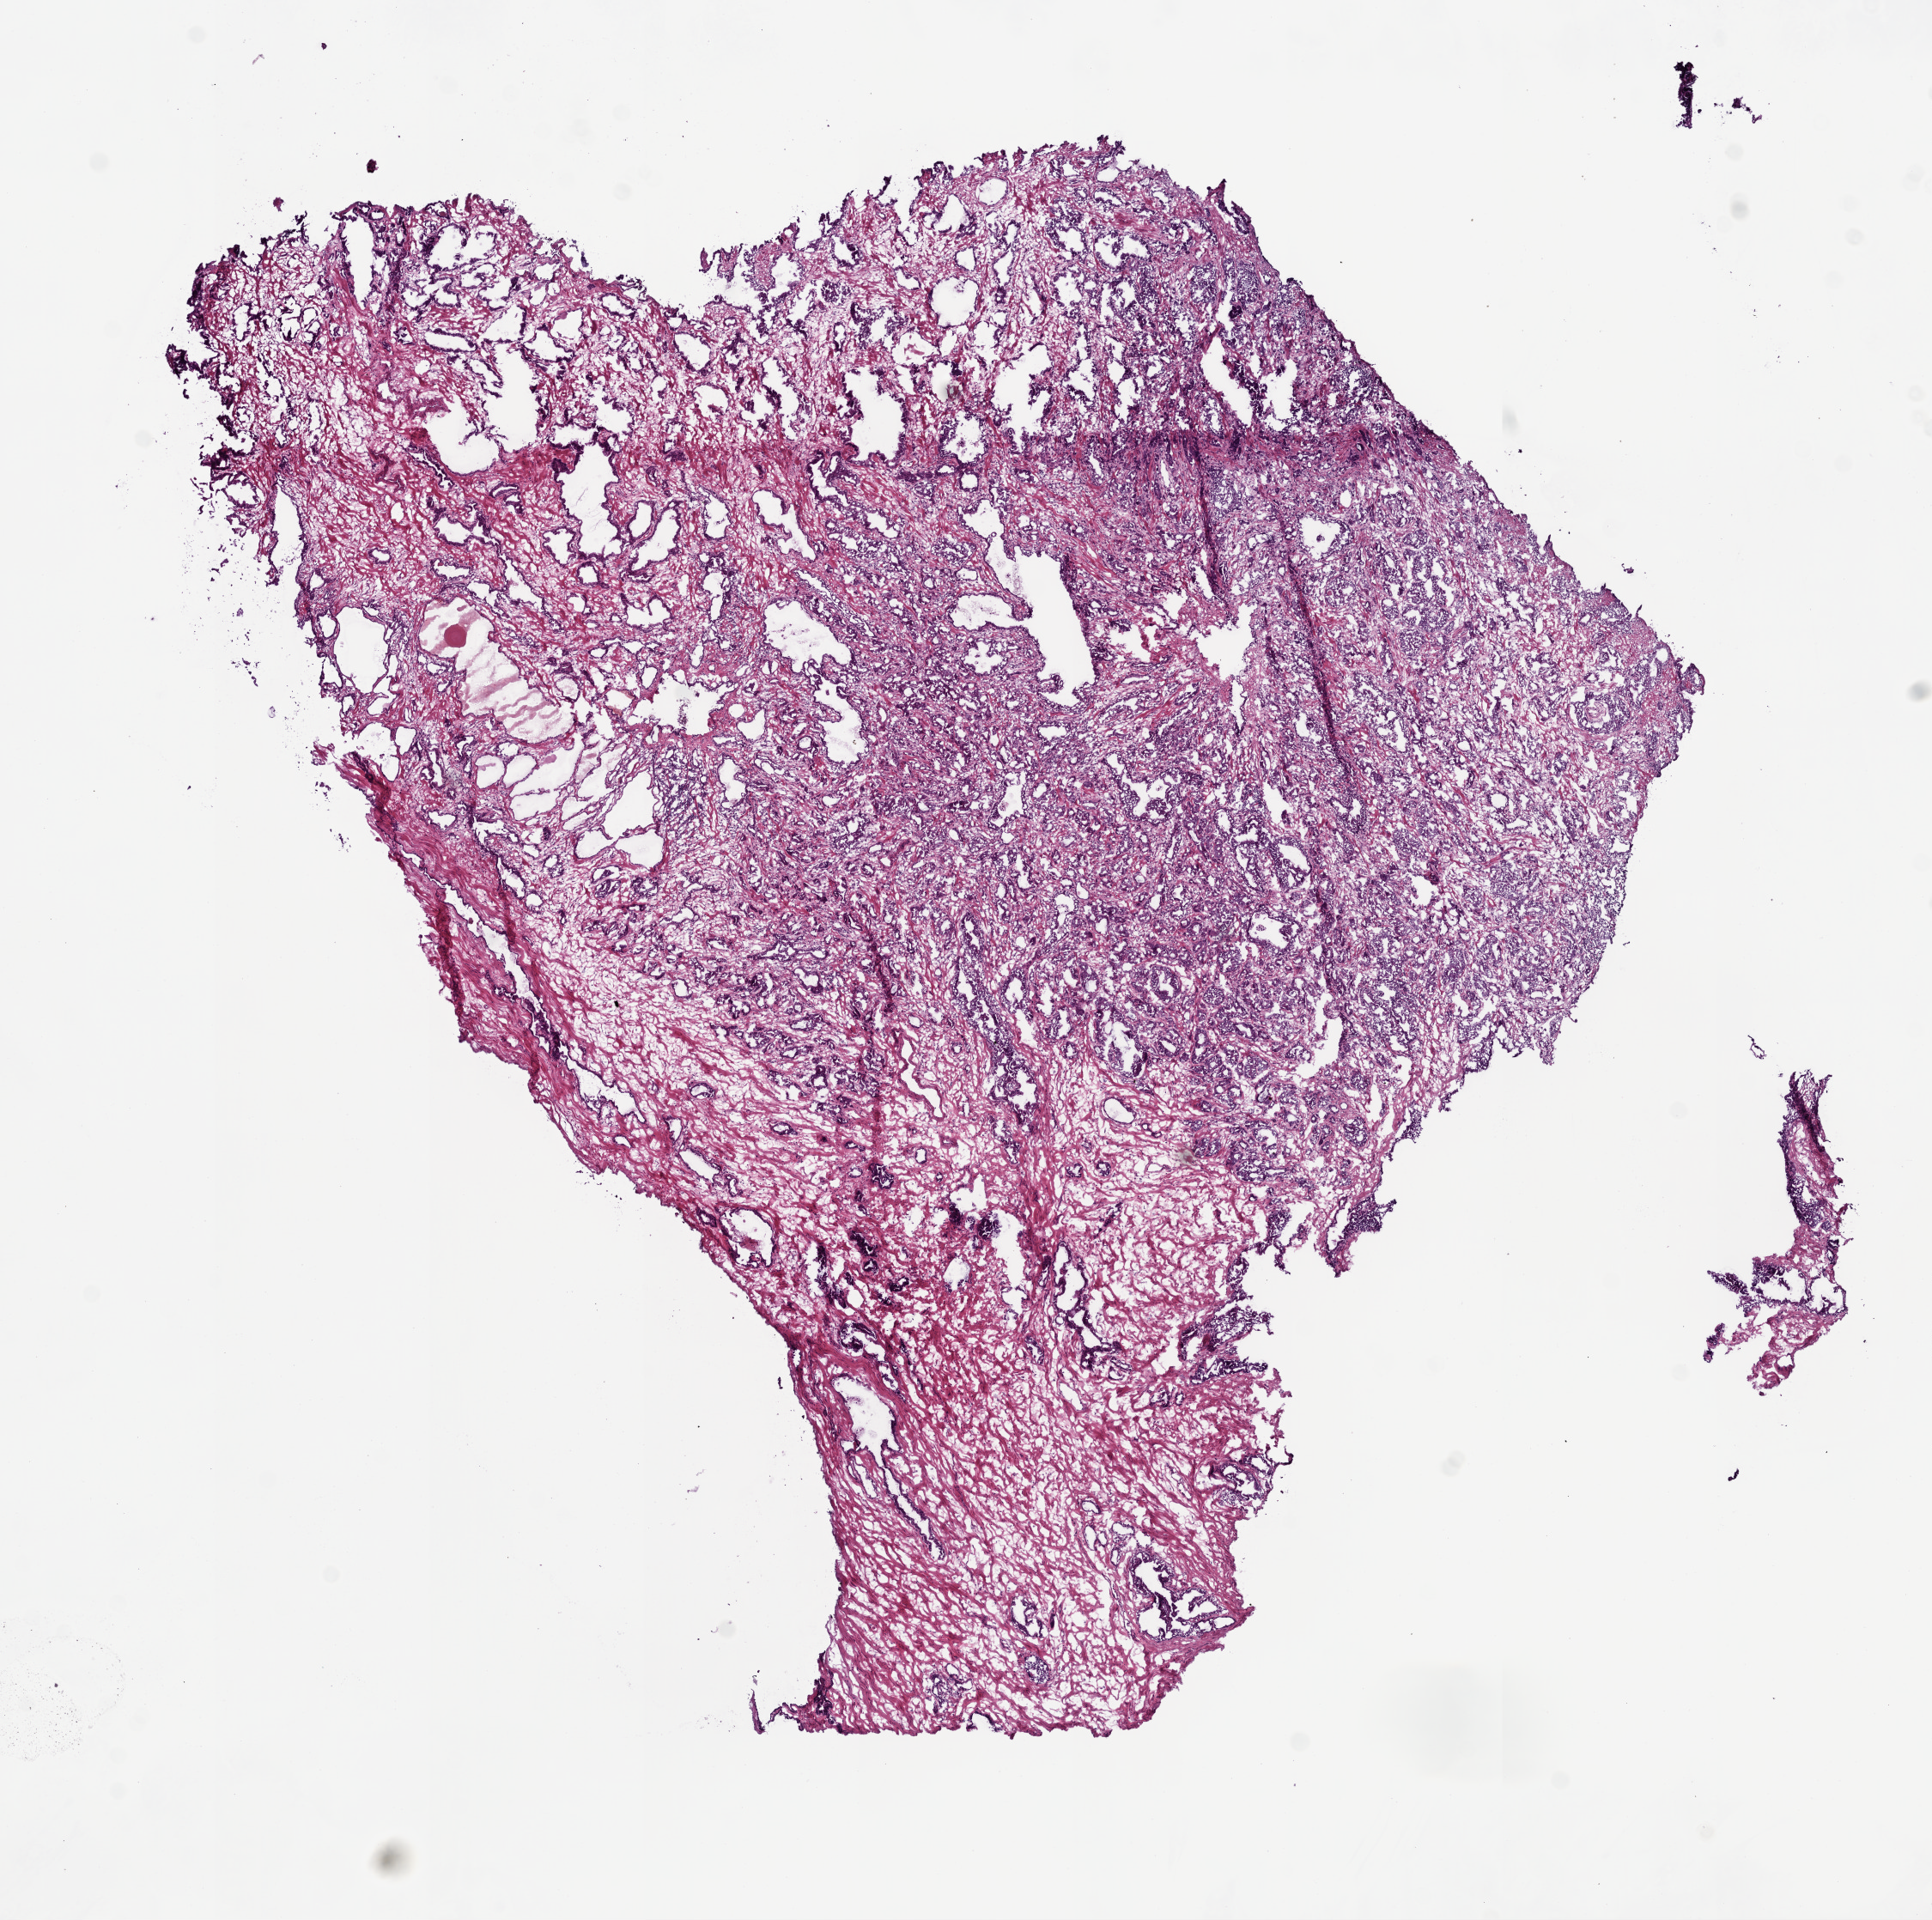
H&E-stained whole-slide image — a low-resolution overview of the entire scanned area, about 9.0 x 9.0 mm (from a 20x scan), frozen section from the top of the tissue portion, primary tumour sample from the prostate. Male patient; age at initial diagnosis 61 years. Gleason score: 7 (4+3). Composition of this section per pathologist review: tumour cells 55%, tumour nuclei 60%, normal cells 20%, stromal cells 25%, necrosis 0%. Infiltration values recorded for this section: lymphocyte infiltration 0%, monocyte infiltration 0%, neutrophil infiltration 0%.
* histologic diagnosis: Acinar cell carcinoma
* lymph nodes positive (case pathology): 0 of 19 examined